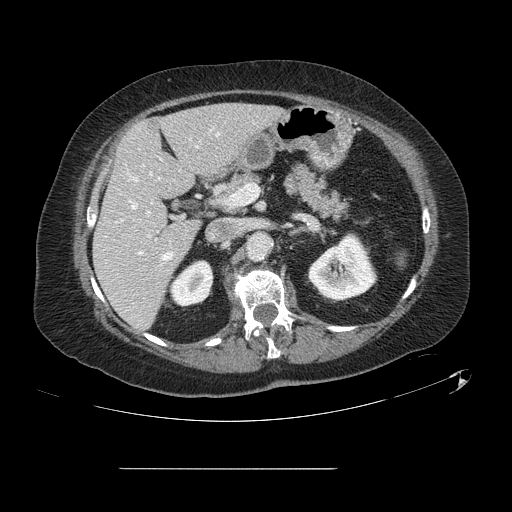
Contrast-enhanced abdominal CT, one axial slice; slice 64 of 148 in the series (ordered by position); 120 kVp; intravenous contrast given; soft-tissue window (W 400 / L 40 HU); 512 × 512 image matrix, field of view 439 × 439 mm. Female patient, age 75 years. Case-level facts recorded for this patient, not image findings: diagnosis: colorectal cancer liver metastases, imaged before liver resection; multiple liver metastases: no; largest metastasis: 2.4 cm; disease in both lobes: no.
Structures marked on this image (outlined manually by an expert reader):
- hepatic veins: bounding box <130,133,219,260> (left, top, right, bottom; pixels)
- liver: <94,104,280,330>
- planned liver remnant (the part of the liver to remain after resection): <94,104,280,330>
- portal vein (with intrahepatic branches): <139,212,150,254>